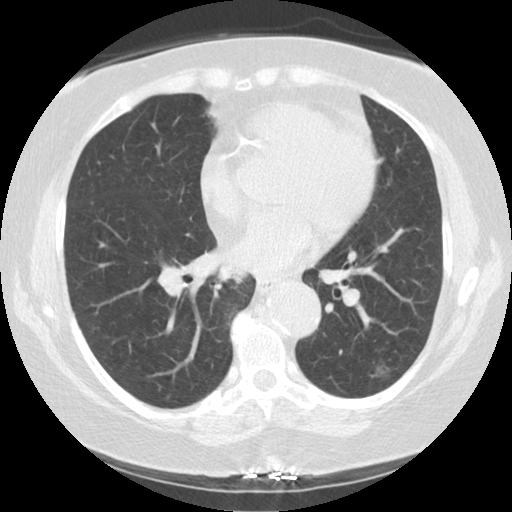
Low-dose screening chest CT, one axial slice; slice 62 of 122 in the series (ordered by position); reconstruction kernel STANDARD; 140 kVp; lung window (W 1500 / L -600 HU); 2.5 mm slice thickness; 512 × 512 image matrix, field of view 329 × 329 mm.
Outlined on this slice (expert manual segmentation):
- lesion 1 (tumor, lower lobe of left lung): bounding box [x1, y1, x2, y2] px = [373, 361, 390, 375]